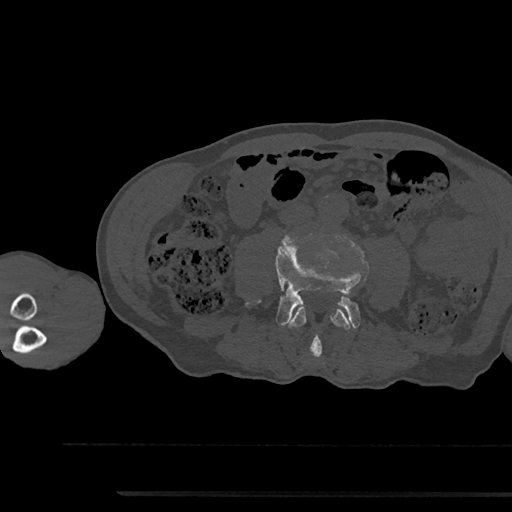
CT including the spine, one axial slice; position 441 of 797 along the scan axis; reconstruction kernel Br40s/3; 120 kVp; bone window (W 1800 / L 400 HU); 512 × 512 image matrix, field of view 367 × 367 mm. Patient: male, 79 years. From the clinical record (not read from this slice): primary cancer: prostate.
Annotated regions visible in this slice (semi-automatically segmented with operator editing):
- L3 vertebra: bounding box [x1, y1, x2, y2] px = [288, 304, 351, 357]
- L4 vertebra: [246, 237, 361, 328]